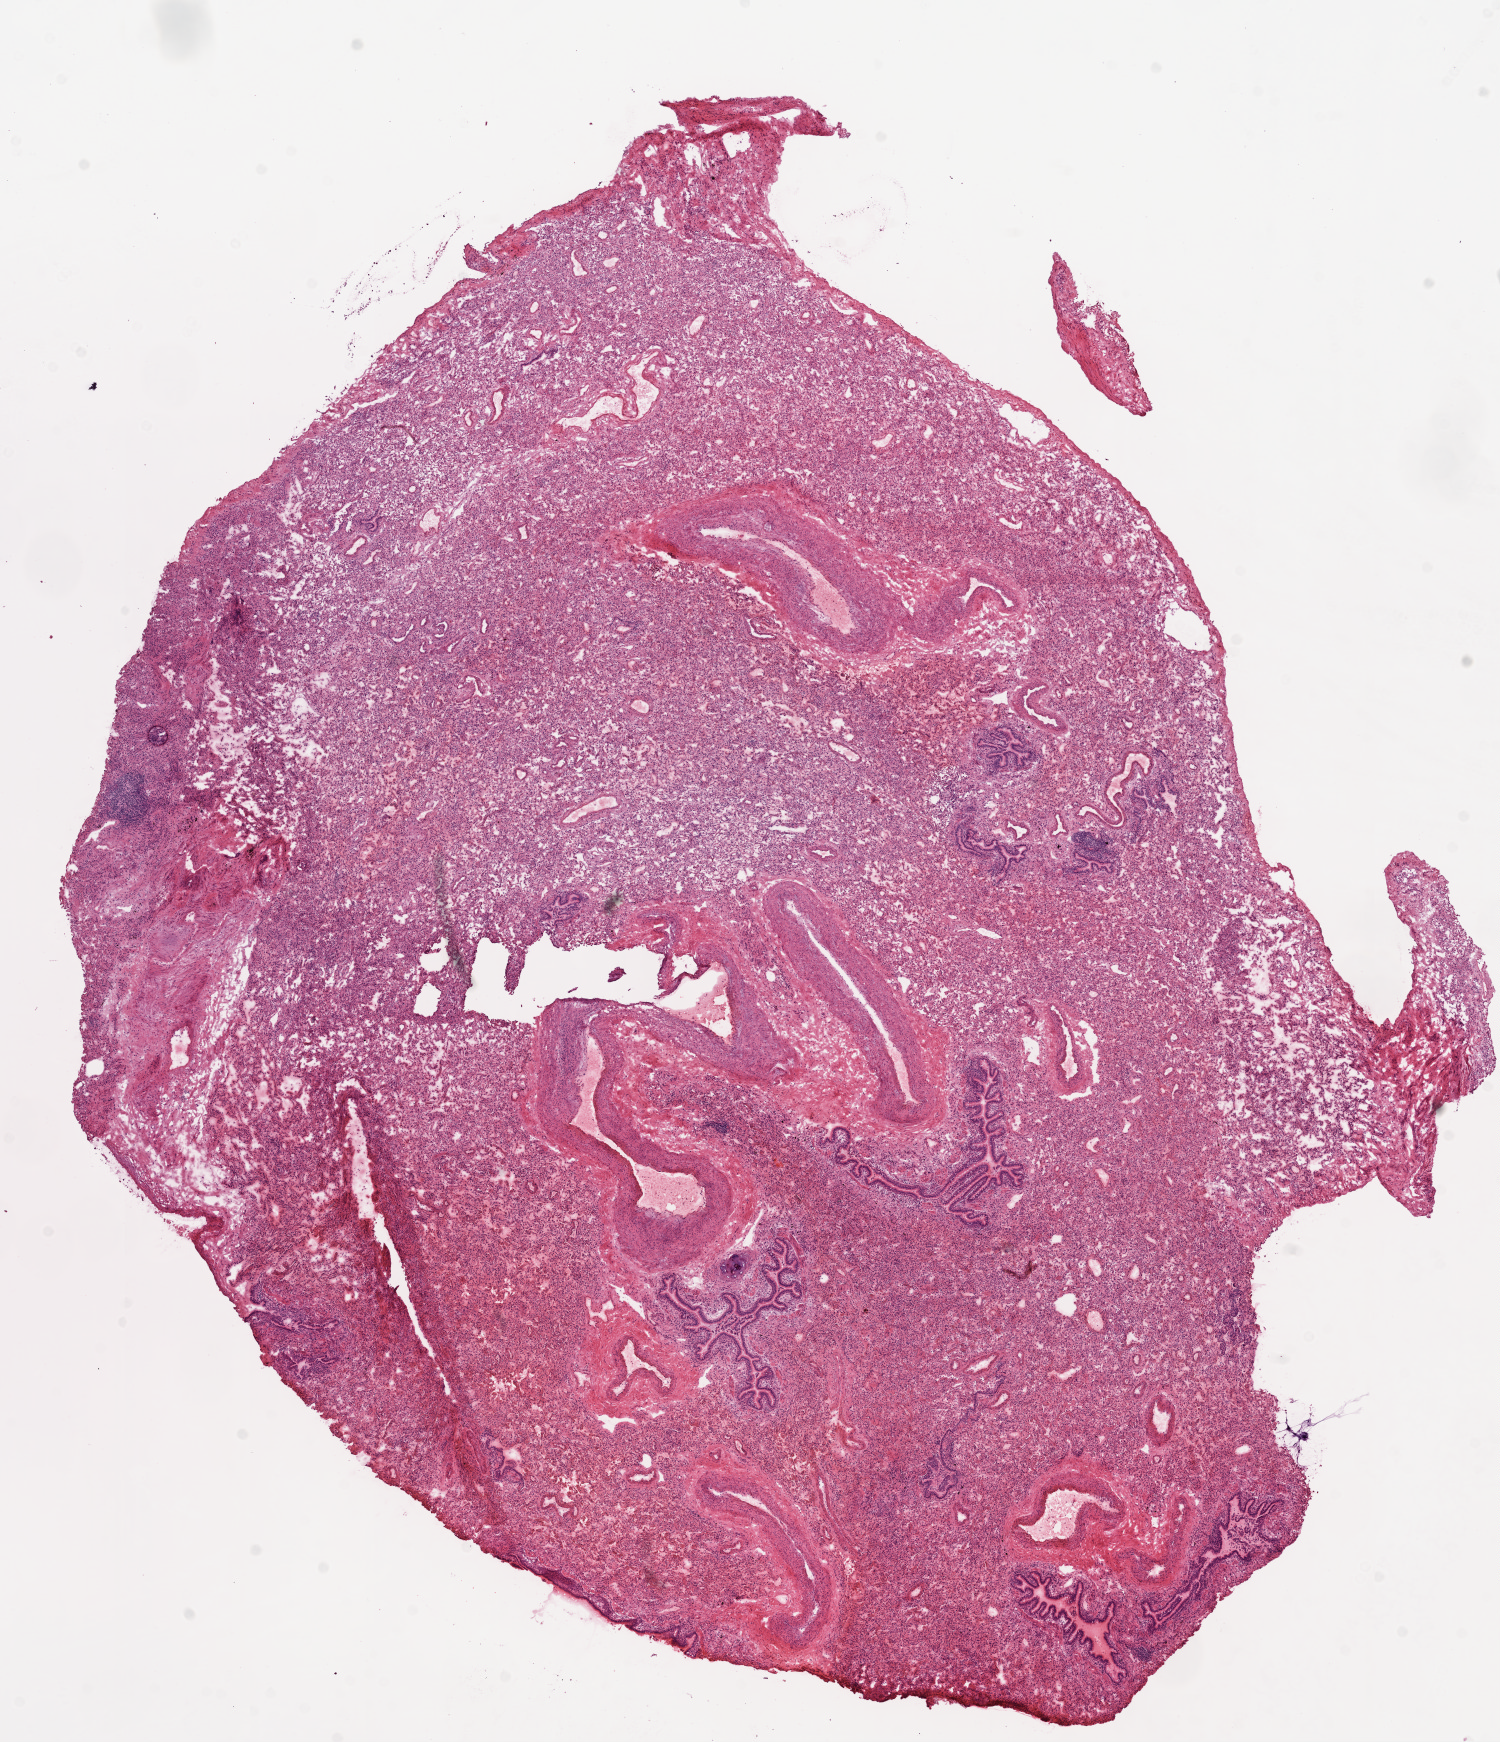
H&E whole-slide image, low-resolution overview of the scanned area, about 12.0 x 14.0 mm. Frozen section. Lung, solid tissue normal (non-tumour tissue) sample. Patient: female, age at initial diagnosis 61 years.
• this section: solid tissue normal sample (biorepository sample class)
• patient diagnosis: Adenocarcinoma, NOS (lower lobe, lung)